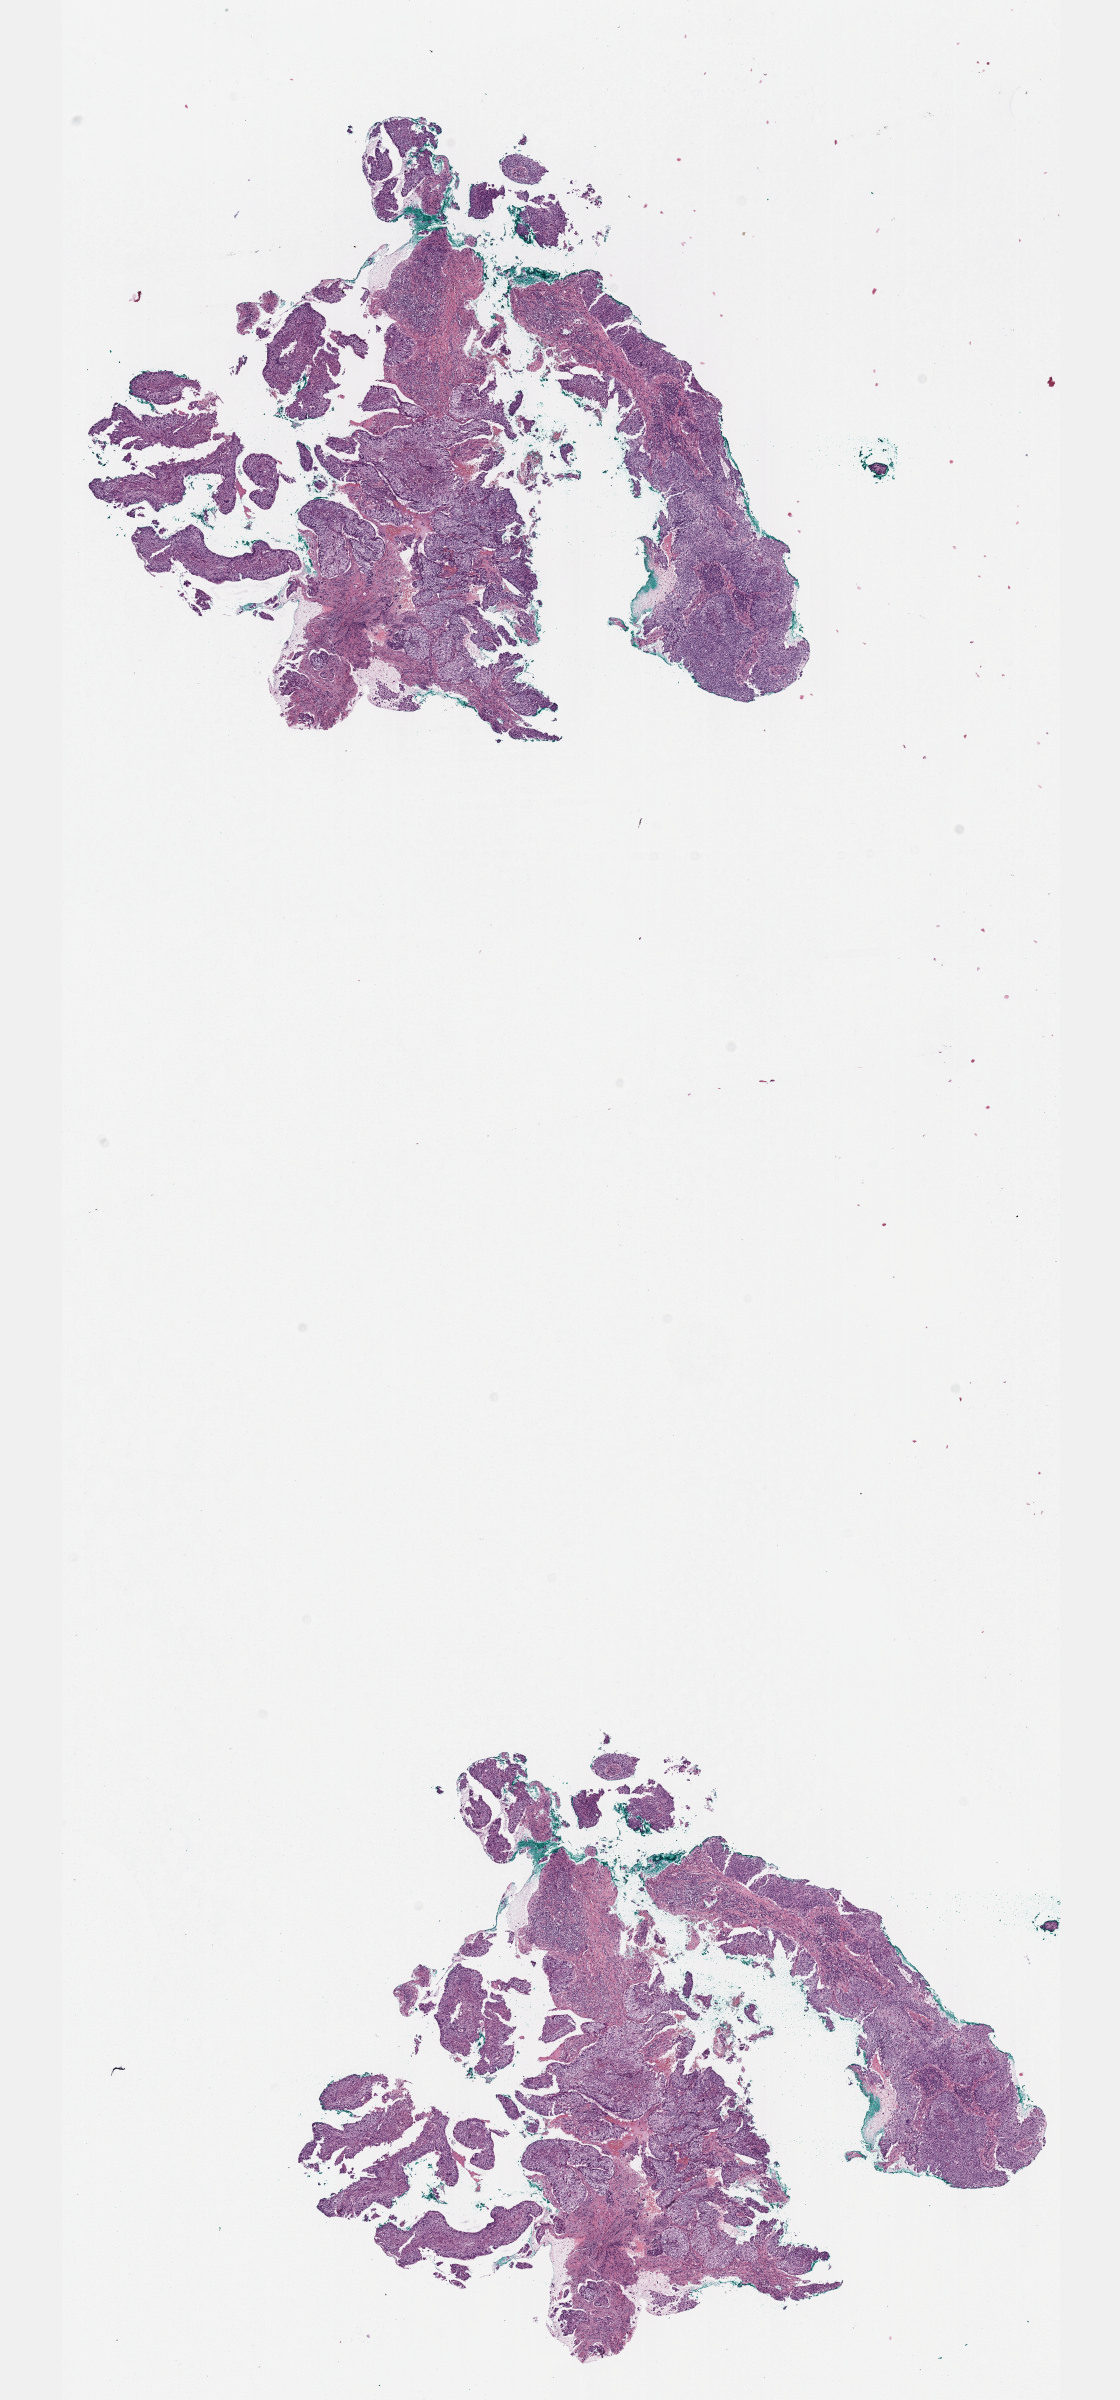
Whole-slide histology image, H&E-stained, whole scanned area (about 9.1 x 19.4 mm, from a 40x scan) shown as a low-resolution overview. Formalin-fixed paraffin-embedded (FFPE) diagnostic section. Sample: primary tumour, cervix. Female, age 65 years at initial diagnosis. Histologic grade: G2 (moderately differentiated).
• histologic diagnosis: Squamous cell carcinoma, NOS (cervix uteri)
• FIGO stage: IVA